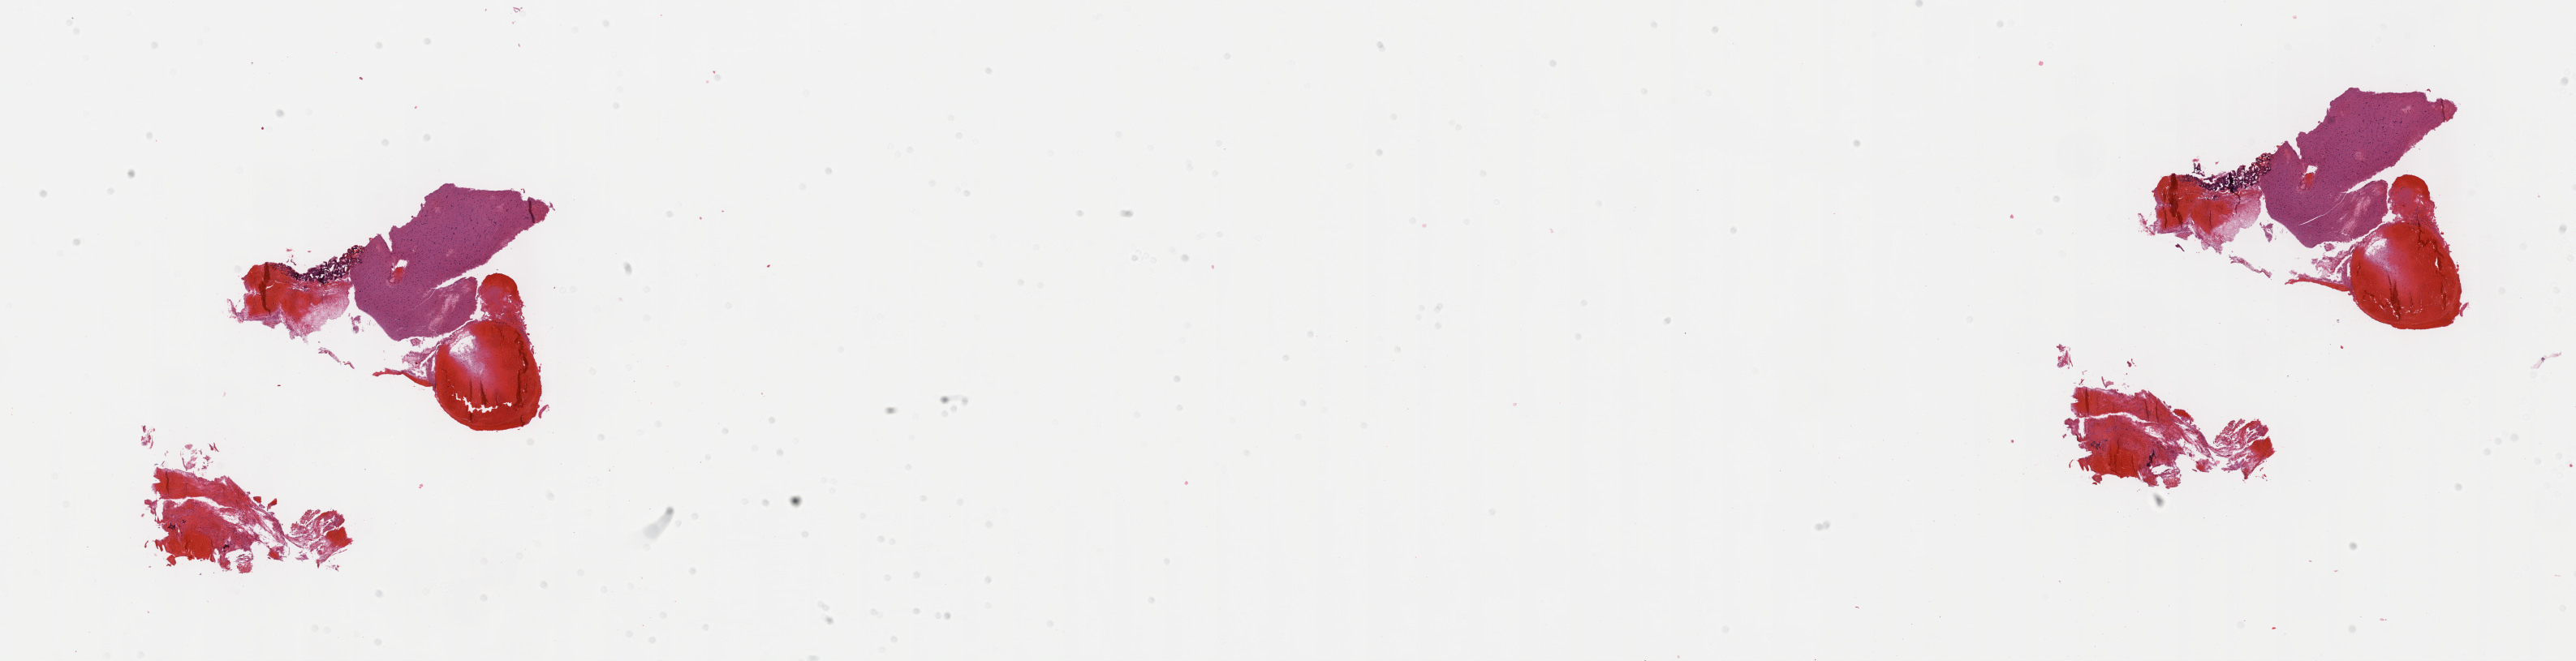
Digitized H&E-stained tissue section (whole slide) — shown as a low-resolution overview of the whole scanned area (about 25.7 x 6.6 mm, from a 40x scan). Formalin-fixed paraffin-embedded (FFPE) diagnostic section. Primary tumour sample from the brain. Patient: female, age at initial diagnosis 18 years. Histologic grade: G2 (moderately differentiated).
Pathologic diagnosis: Mixed glioma. Laterality: left.